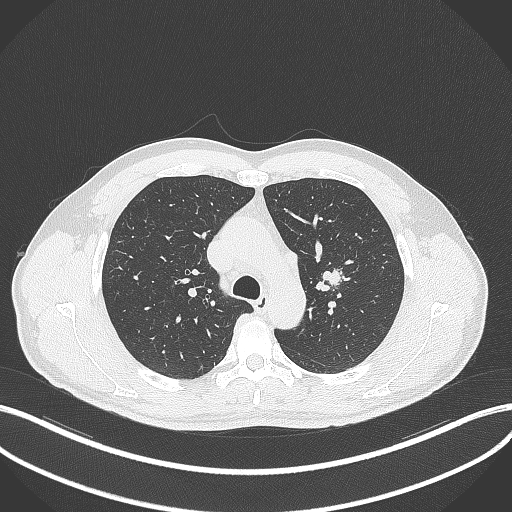
Chest CT, one axial slice. Position 300 of 392 along the scan axis. Reconstruction kernel B70f. 120 kVp. Lung window (W 1500 / L -600 HU). 512 × 512 image matrix. Male patient, age 50 years. From the clinical record (not read from this slice): clinical TNM (as recorded): T1c N1 M1b.
Outlined on this slice (bounding box drawn by a radiologist):
- lung tumour (recorded histology: squamous cell carcinoma): box from (x=312, y=268) to (x=343, y=295) px